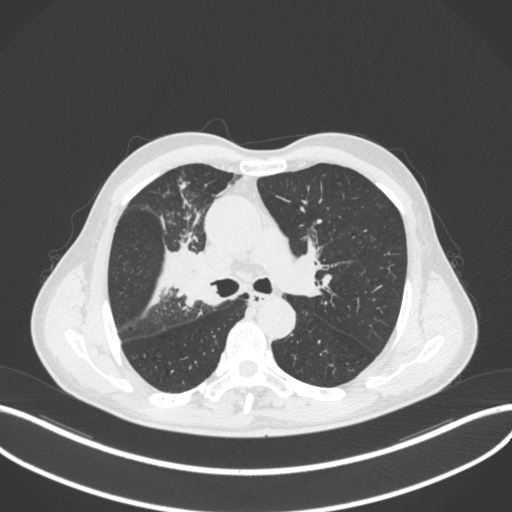
Chest CT, one axial slice. Slice 310 of 490 in the series (ordered by position). Reconstruction kernel B31f. 120 kVp. Lung window (W 1500 / L -600 HU). 1 mm slice thickness. 512 × 512 image matrix, field of view 400 × 400 mm. Patient: male, 69 years. From the clinical record (not read from this slice): clinical TNM (as recorded): T2a N0 M0.
Structures marked on this image (bounding box drawn by a radiologist):
- lung tumour (recorded histology: adenocarcinoma): bounding box (x1, y1, x2, y2) in pixels: (168, 255, 214, 309)